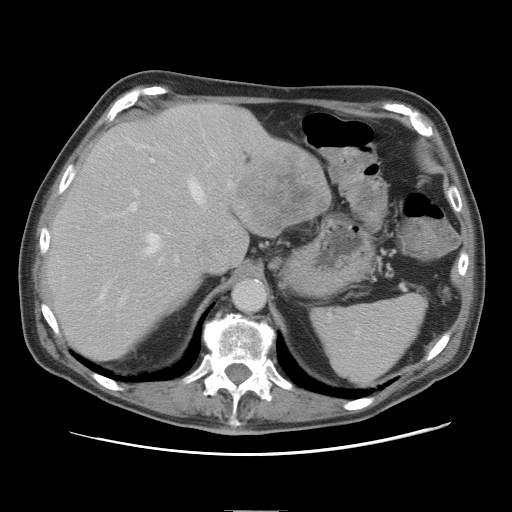
Contrast-enhanced abdominal CT, one axial slice. Position 57 of 89 along the scan axis. 120 kVp. Intravenous contrast given. Soft-tissue window (W 400 / L 40 HU). 5 mm slice thickness. 512 × 512 image matrix, field of view 375 × 375 mm. Male patient, age 69 years. Case-level facts recorded for this patient, not image findings: diagnosis: colorectal cancer liver metastases, imaged before liver resection; multiple liver metastases: no; largest metastasis: 8.5 cm; disease in both lobes: no.
Annotated regions visible in this slice (outlined manually by an expert reader):
- hepatic veins: bounding box <101,175,206,298> (left, top, right, bottom; pixels)
- liver: <47,103,329,359>
- planned liver remnant (the part of the liver to remain after resection): <48,102,245,359>
- portal vein (with intrahepatic branches): <122,141,231,301>
- liver metastasis: <237,157,327,235>